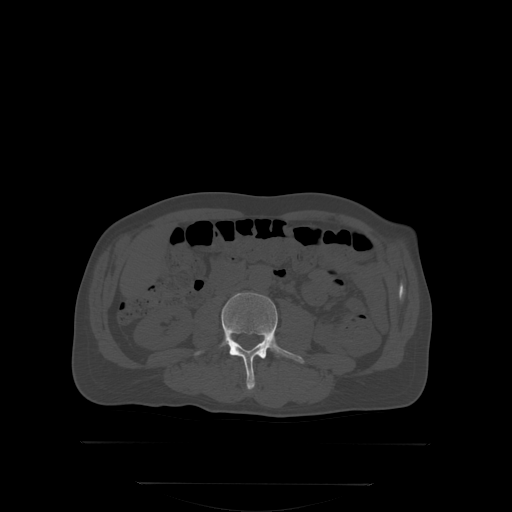
CT including the spine, one axial slice; slice 122 of 350 in the series (ordered by position); bone window (W 1800 / L 400 HU); 2.5 mm slice thickness; 512 × 512 image matrix, field of view 500 × 500 mm. Male patient, age 58 years. Case-level facts recorded for this patient, not image findings: primary cancer: prostate; vertebrae with lytic lesions (as recorded): L1.
Annotated regions visible in this slice (semi-automatic segmentation, software-assisted and operator-edited):
- L3 vertebra: box from (x=194, y=292) to (x=305, y=390) px